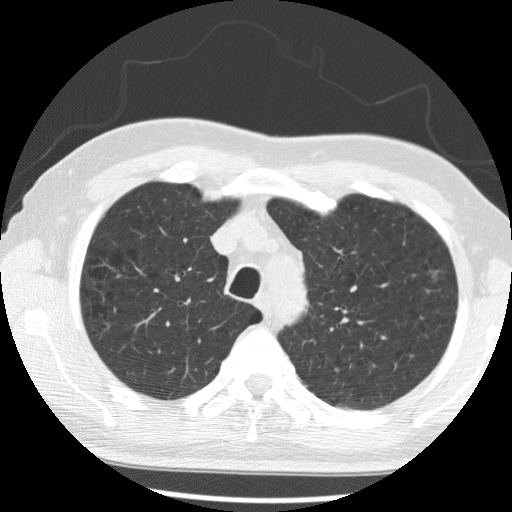
Axial slice from a low-dose chest CT screening exam, second screening round (one year after baseline), lung window (W 1500 / L -600 HU), 2.5 mm slice thickness. Male, age 68 years at enrolment.
Expert-annotated lung lesion, bounding box <412,257,461,295> (left, top, right, bottom; pixels). Reader record for this screening exam (exam-level; its link to the box is not recorded): non-calcified nodule or mass ≥4 mm, left upper lobe, 15 × 11 mm, poorly defined margins, ground glass attenuation, pre-existing on the prior screen: yes; interval growth: yes. Later outcome: lung cancer diagnosed 278 days after this screen — bronchiolo-alveolar adenocarcinoma, NOS, left upper lobe, moderately differentiated (G2), stage IA (AJCC 6th edition), 17 mm at pathology.